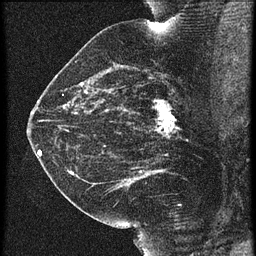
Breast MRI (dynamic contrast-enhanced), one sagittal slice. Slice 34 of 60 in the series (ordered by position). 3 images stored at this slice position (order not interpretable as contrast timing). 1.5 T. TE 4.2 ms, TR 21.3 ms. 1.5 mm slice thickness. 256 × 256 image matrix, field of view 180 × 180 mm. Patient: female, 42 years. Case-level facts recorded for this patient, not image findings: setting: breast cancer imaged before/during neoadjuvant chemotherapy; receptor status: HER2-positive.
Annotated regions visible in this slice (semi-automatic segmentation, software-assisted and operator-edited):
- analysis volume of interest (the breast-tissue region the enhancement analysis was run in; not a lesion): box from (x=122, y=82) to (x=195, y=147) px
- tumour enhancement mask (voxels above the 90 % enhancement threshold inside the analysis volume of interest): (x=154, y=100)–(x=175, y=133)